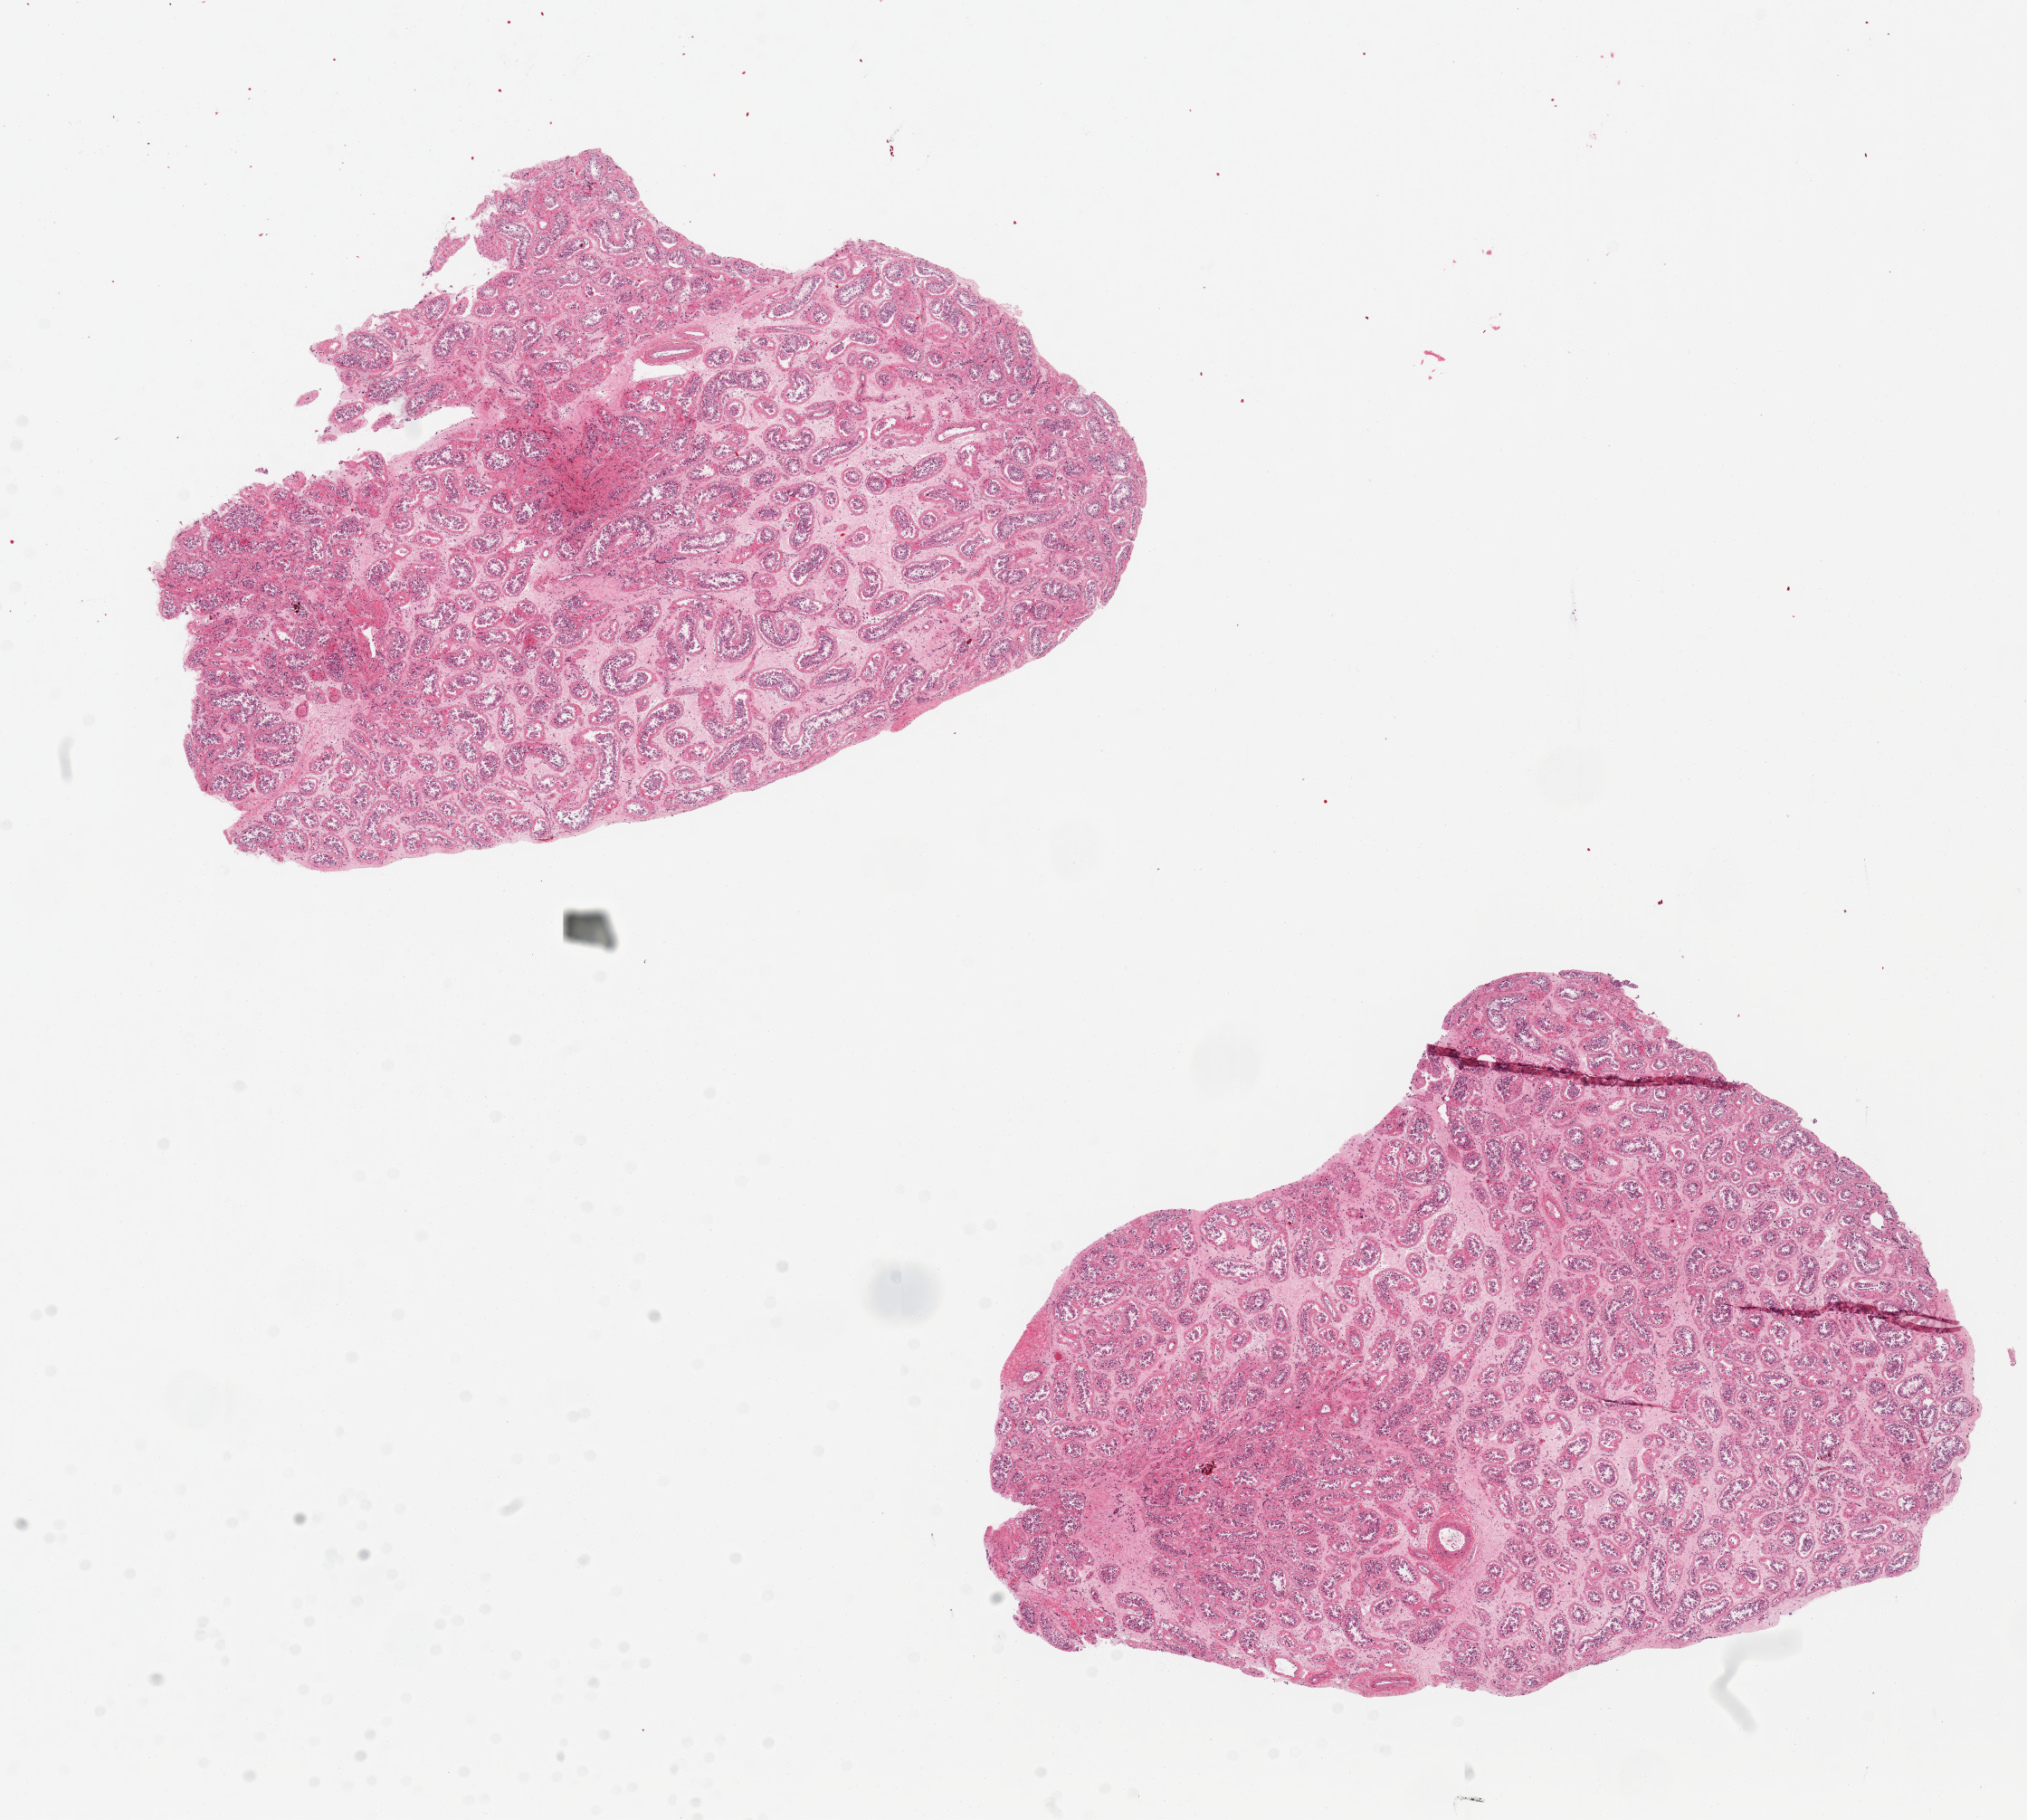
Whole-slide image, hematoxylin and eosin (H&E) stain — a low-resolution overview of the entire scanned area, about 17.7 x 15.9 mm; PAXgene-fixed paraffin-embedded (PFPE) section; section of testis (target tissue); tissue donor sample. Male donor.
Reviewer comment on this tissue sample: 2 pieces, 9x6 & 9x6mm; Reduced spermatogenesis.